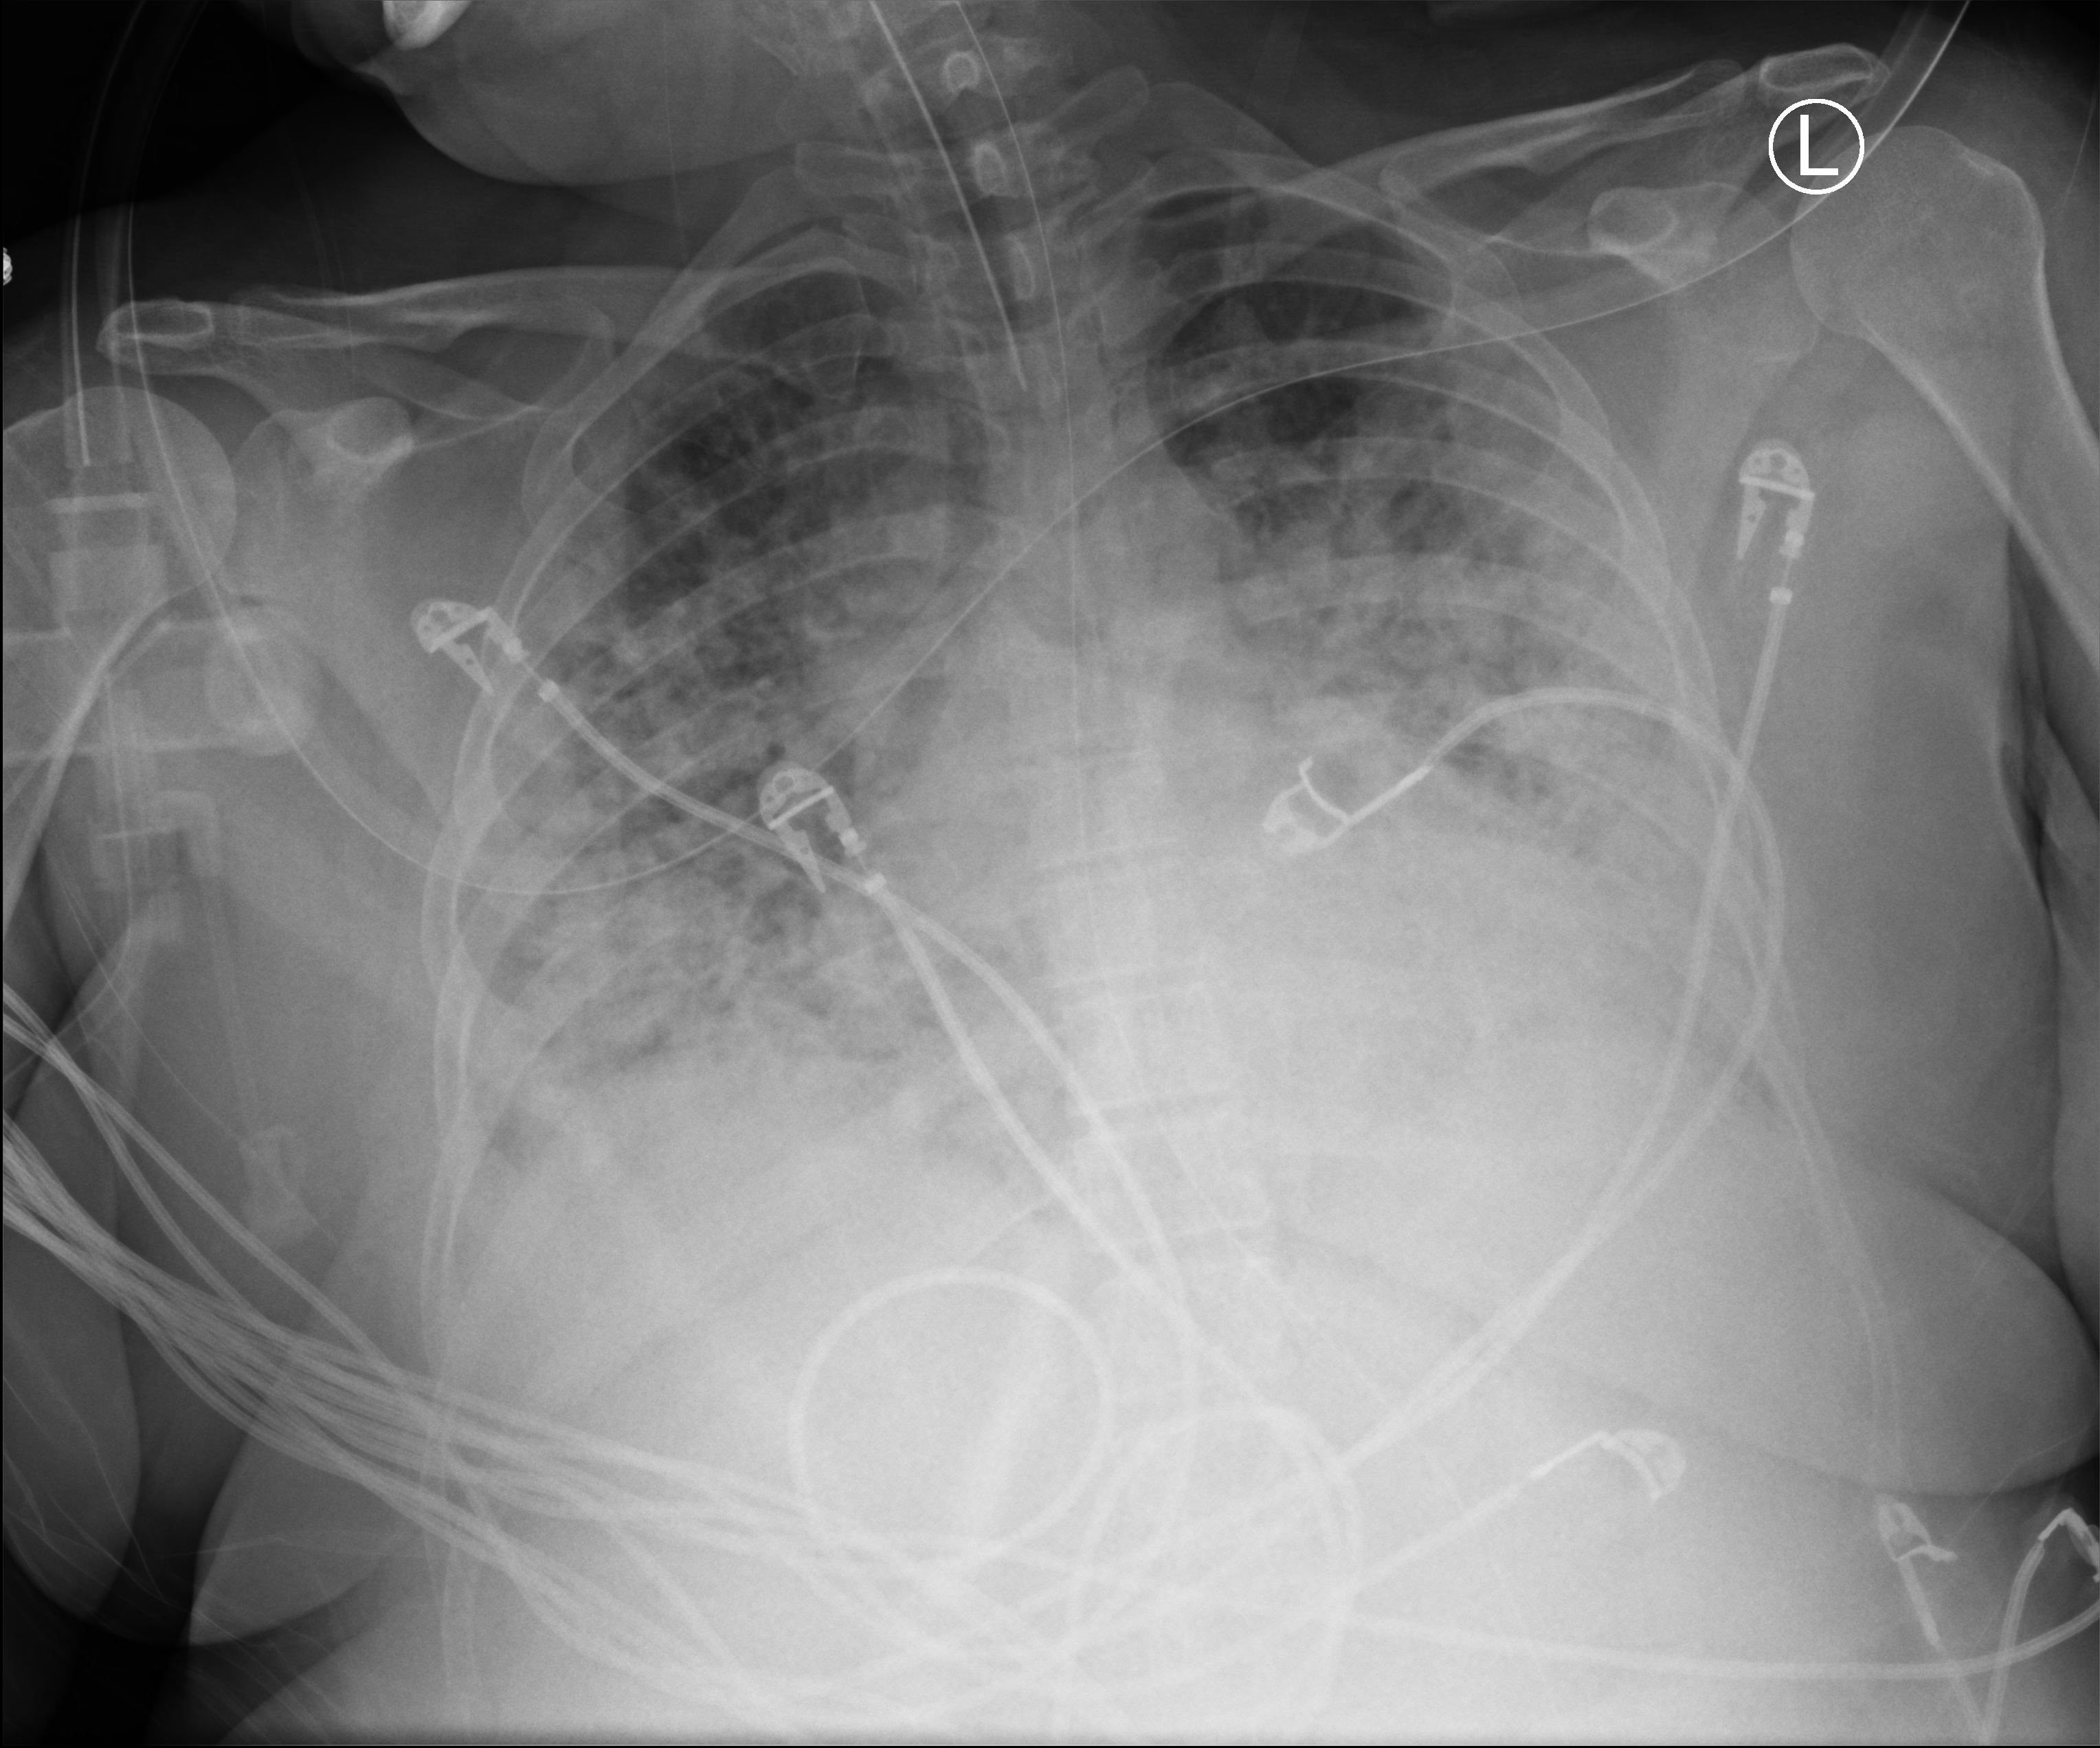
Portable chest radiograph. Female patient hospitalised with COVID-19, age 18–59 years.
Hospital-stay facts (about this admission, not read from this image; timing relative to this image not recorded): smoking status (admission record): never; mechanically ventilated during this hospital stay: yes.